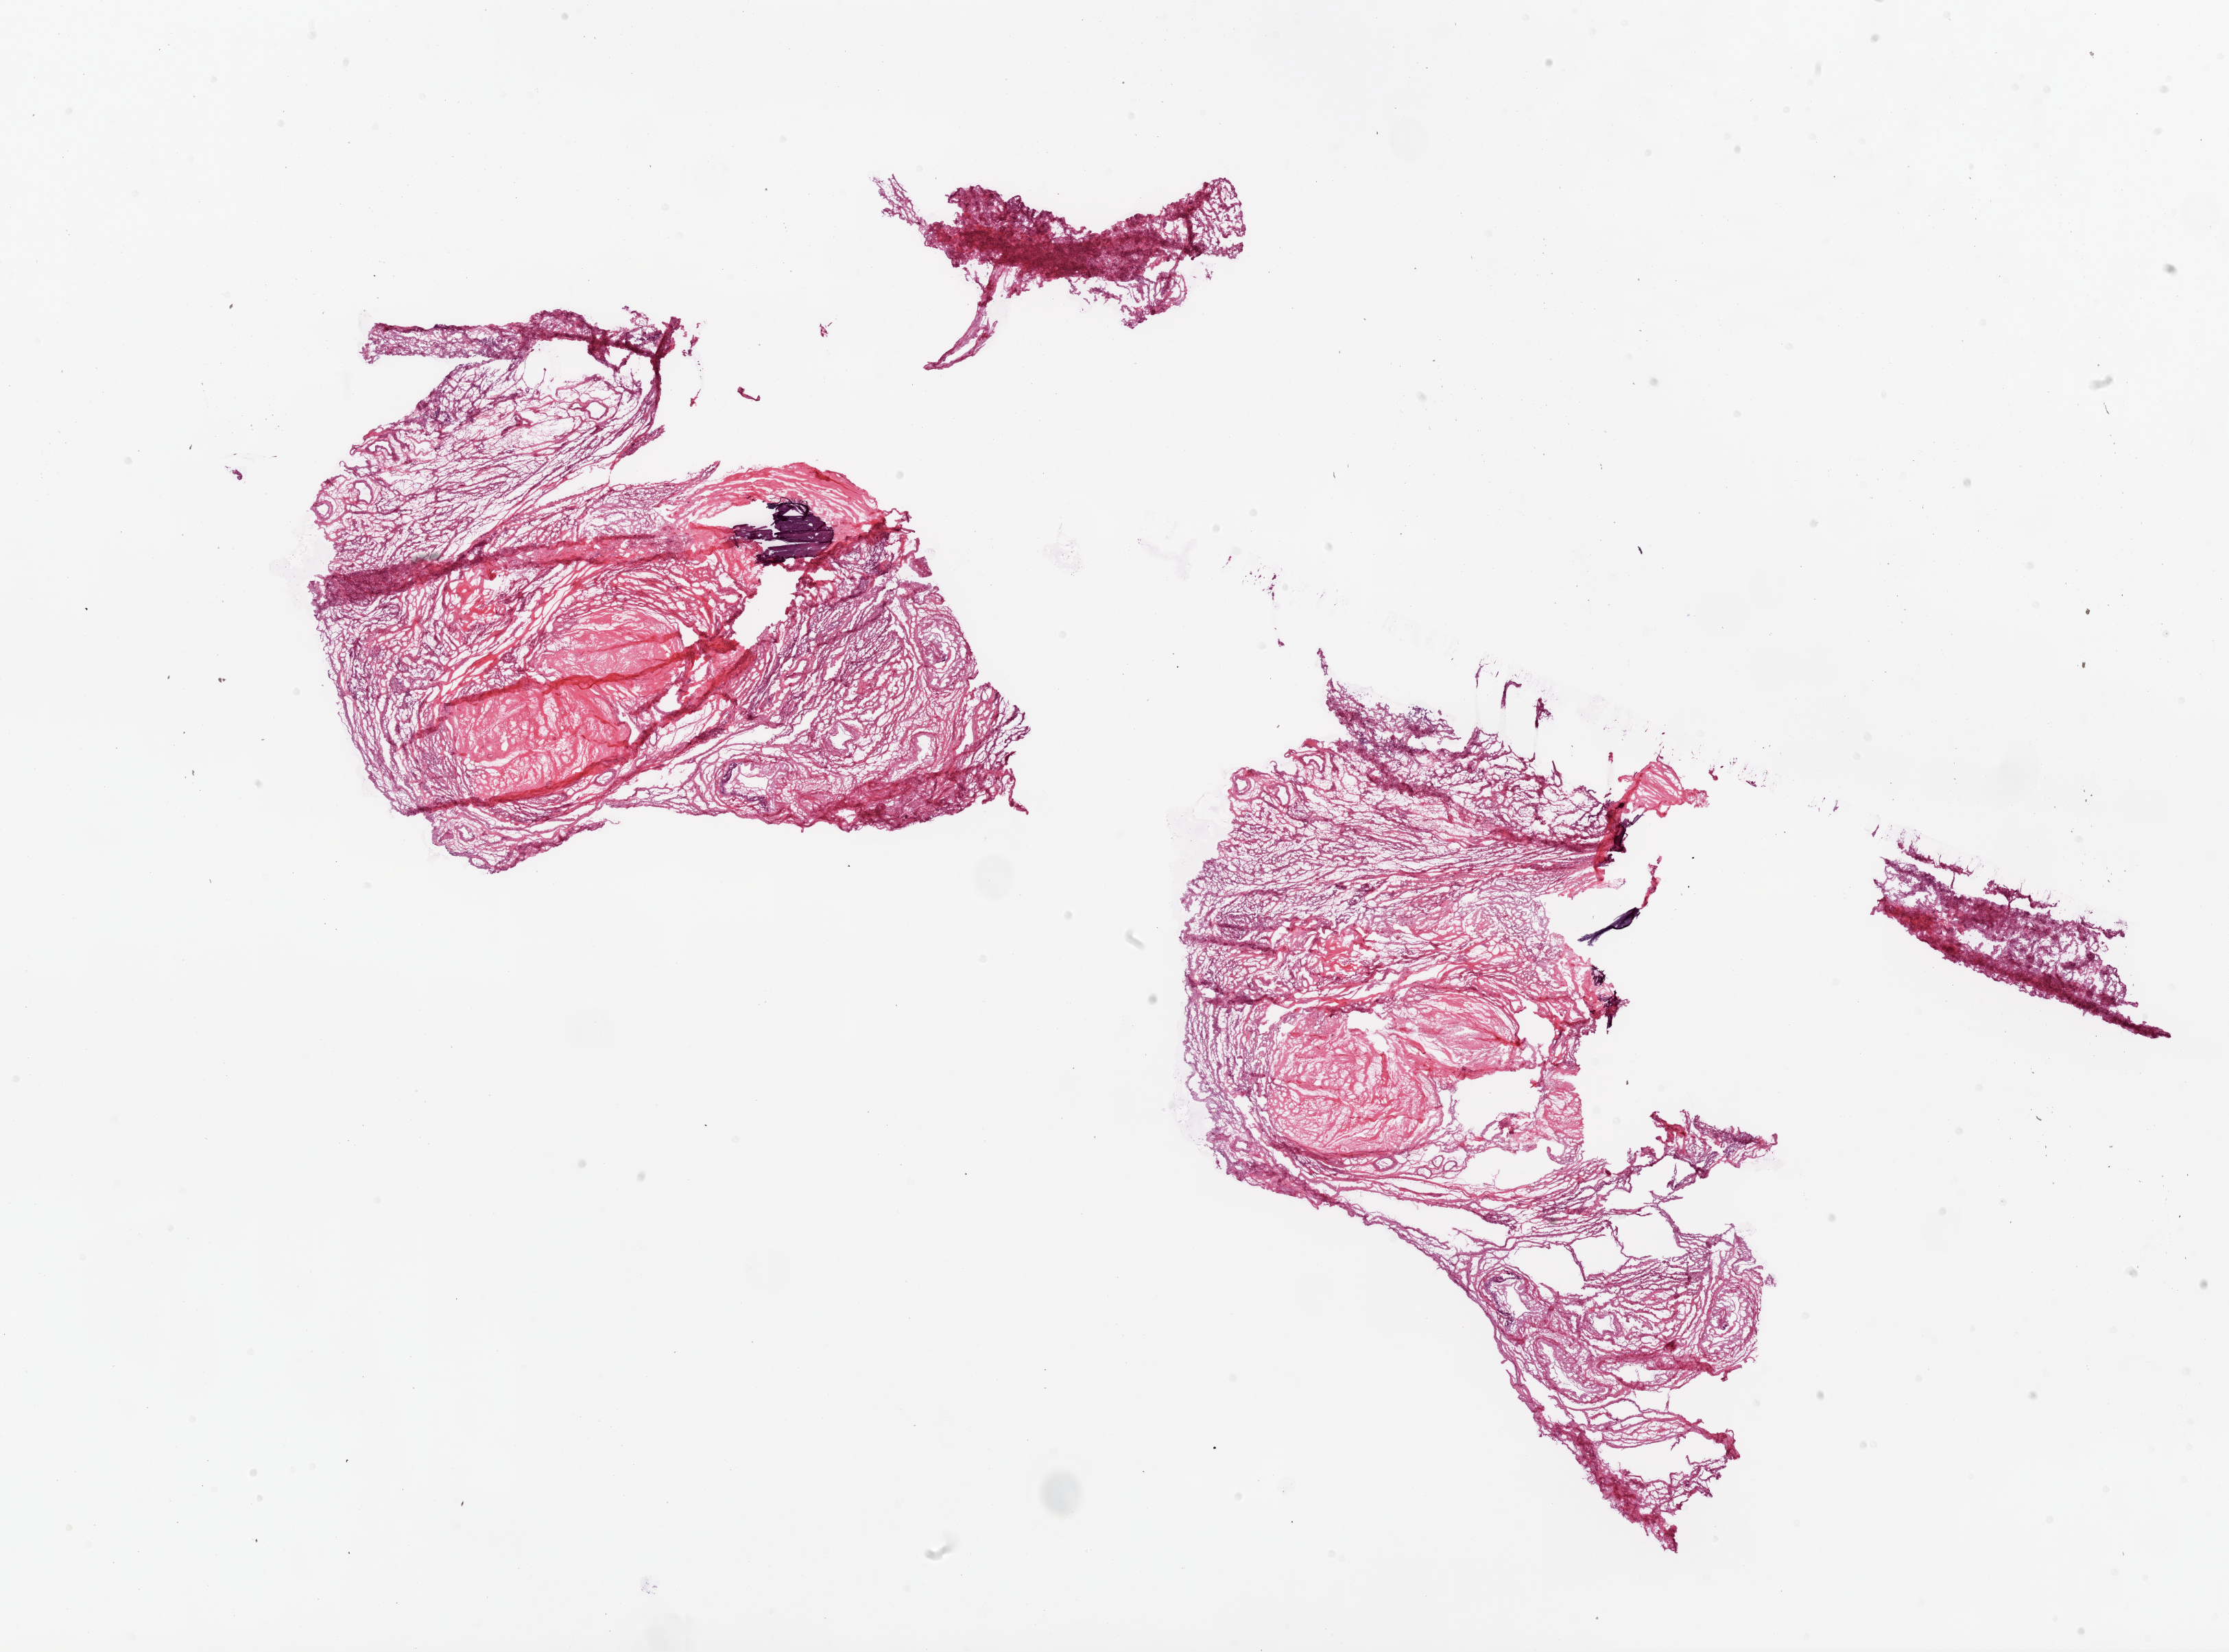
Hematoxylin and eosin (H&E) stained whole-slide image — shown as a low-resolution overview of the whole scanned area (about 26.1 x 19.3 mm), frozen section, ovary, solid tissue normal (non-tumour tissue) sample. Female, age 72 years at initial diagnosis.
This section: solid tissue normal sample (biorepository sample class). Patient diagnosis: Serous cystadenocarcinoma, NOS.